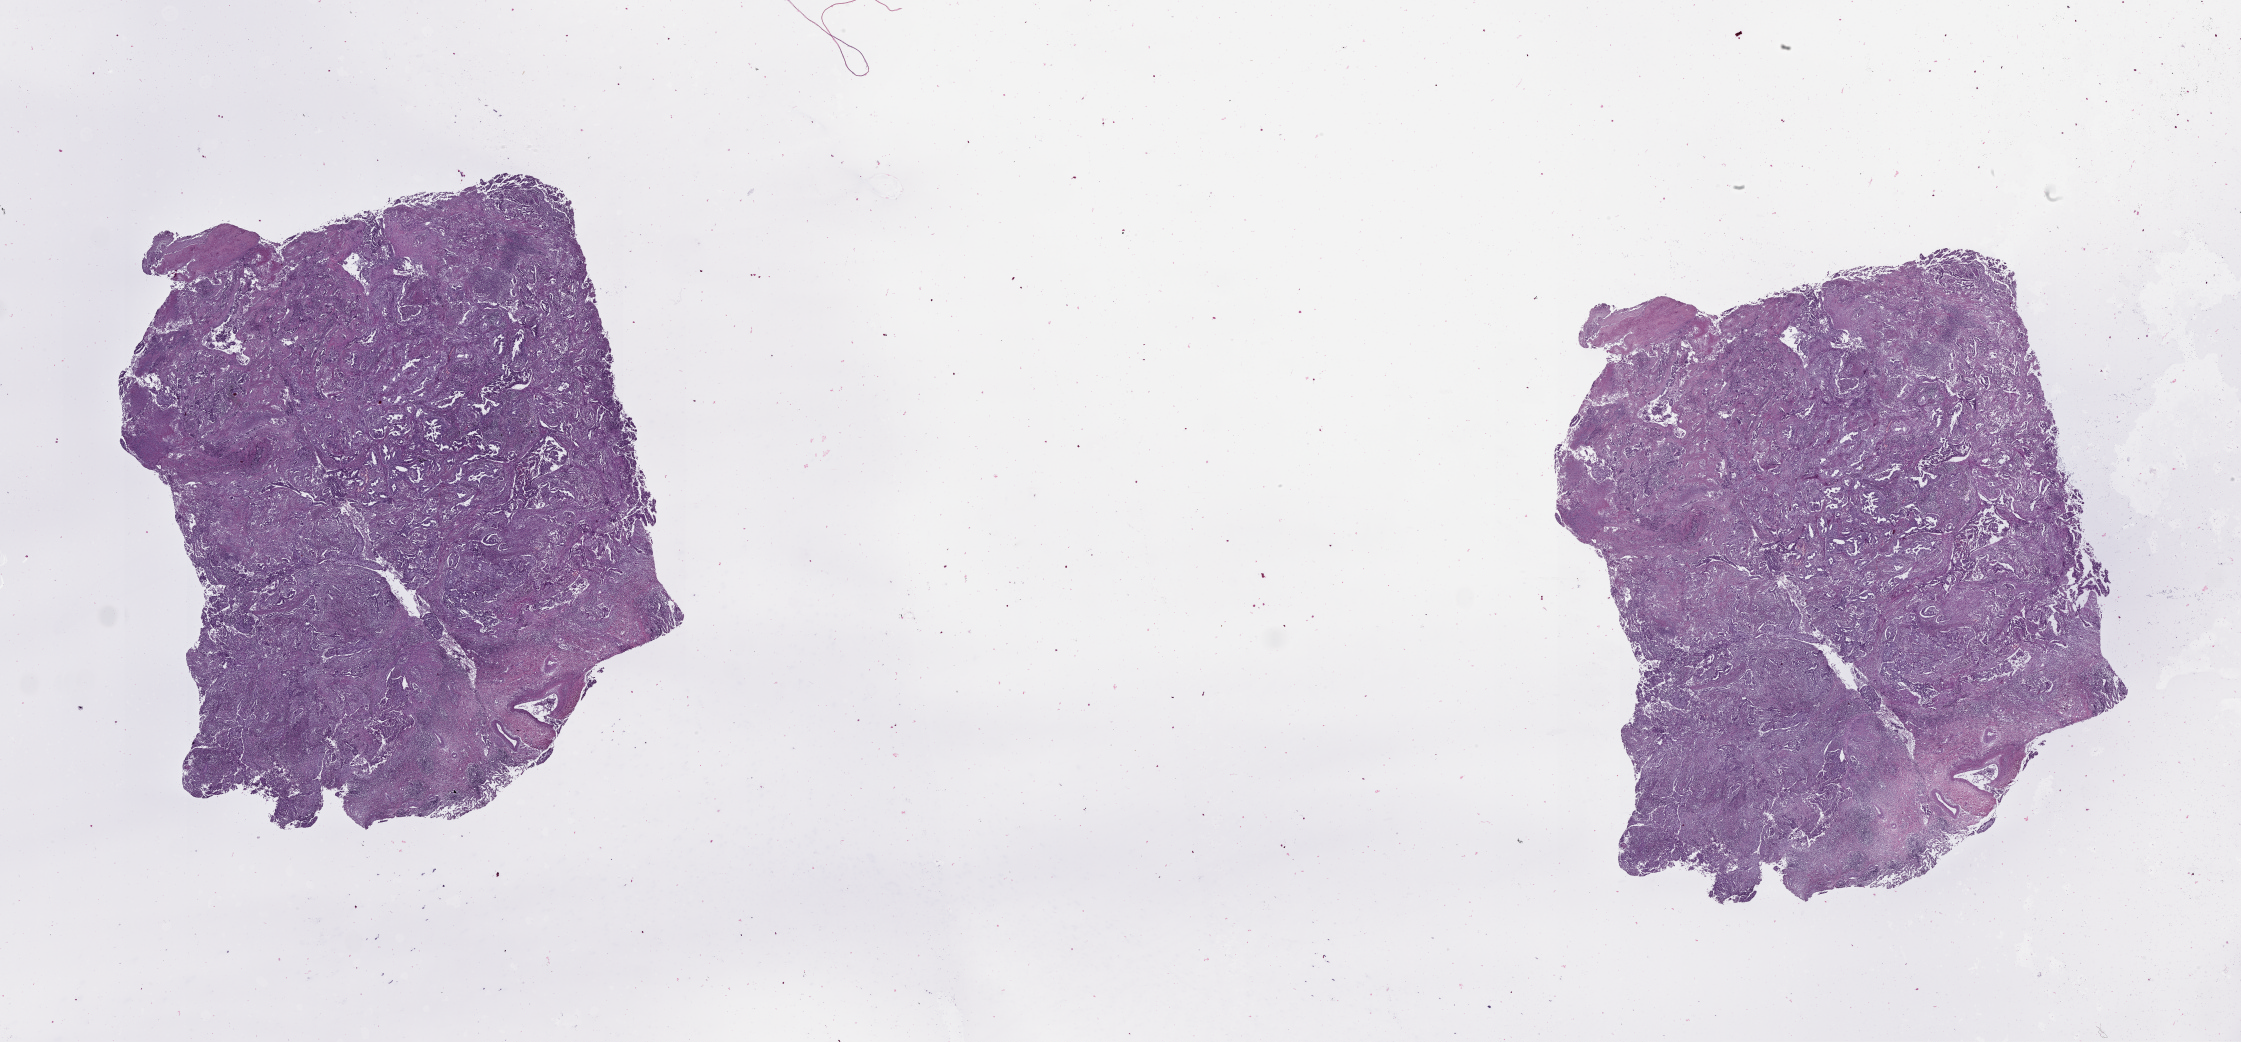
H&E-stained whole-slide image — shown as a low-resolution overview of the whole scanned area (about 36.1 x 16.8 mm); lung, tissue type not recorded.
* patient diagnosis (cohort enrolment): lung adenocarcinoma (lung)